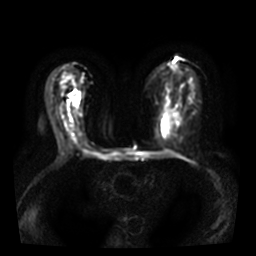
Breast MRI, one axial slice; slice 17 of 38 in the series (ordered by position); diffusion-weighted series; image 2 of 4 stored at this slice position (different b-values; order by instance number); 3 T; 5 mm slice thickness; 256 × 256 image matrix, field of view 320 × 320 mm. Female patient.
Outlined on this slice (expert manual segmentation):
- tumour on diffusion-weighted imaging: bounding box <75,97,78,102> (left, top, right, bottom; pixels)